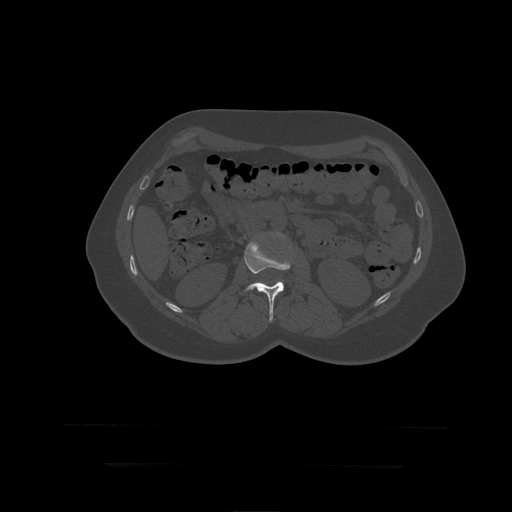
CT including the spine, one axial slice. Slice 144 of 399 in the series (ordered by position). Reconstruction kernel STANDARD. Bone window (W 1800 / L 400 HU). 512 × 512 image matrix, field of view 450 × 450 mm. Patient age 41 years. Case-level facts recorded for this patient, not image findings: primary cancer: breast.
Structures marked on this image (semi-automatically segmented with operator editing):
- L2 vertebra: bounding box (x1, y1, x2, y2) in pixels: (244, 241, 291, 322)
- L3 vertebra: (276, 233, 284, 237)